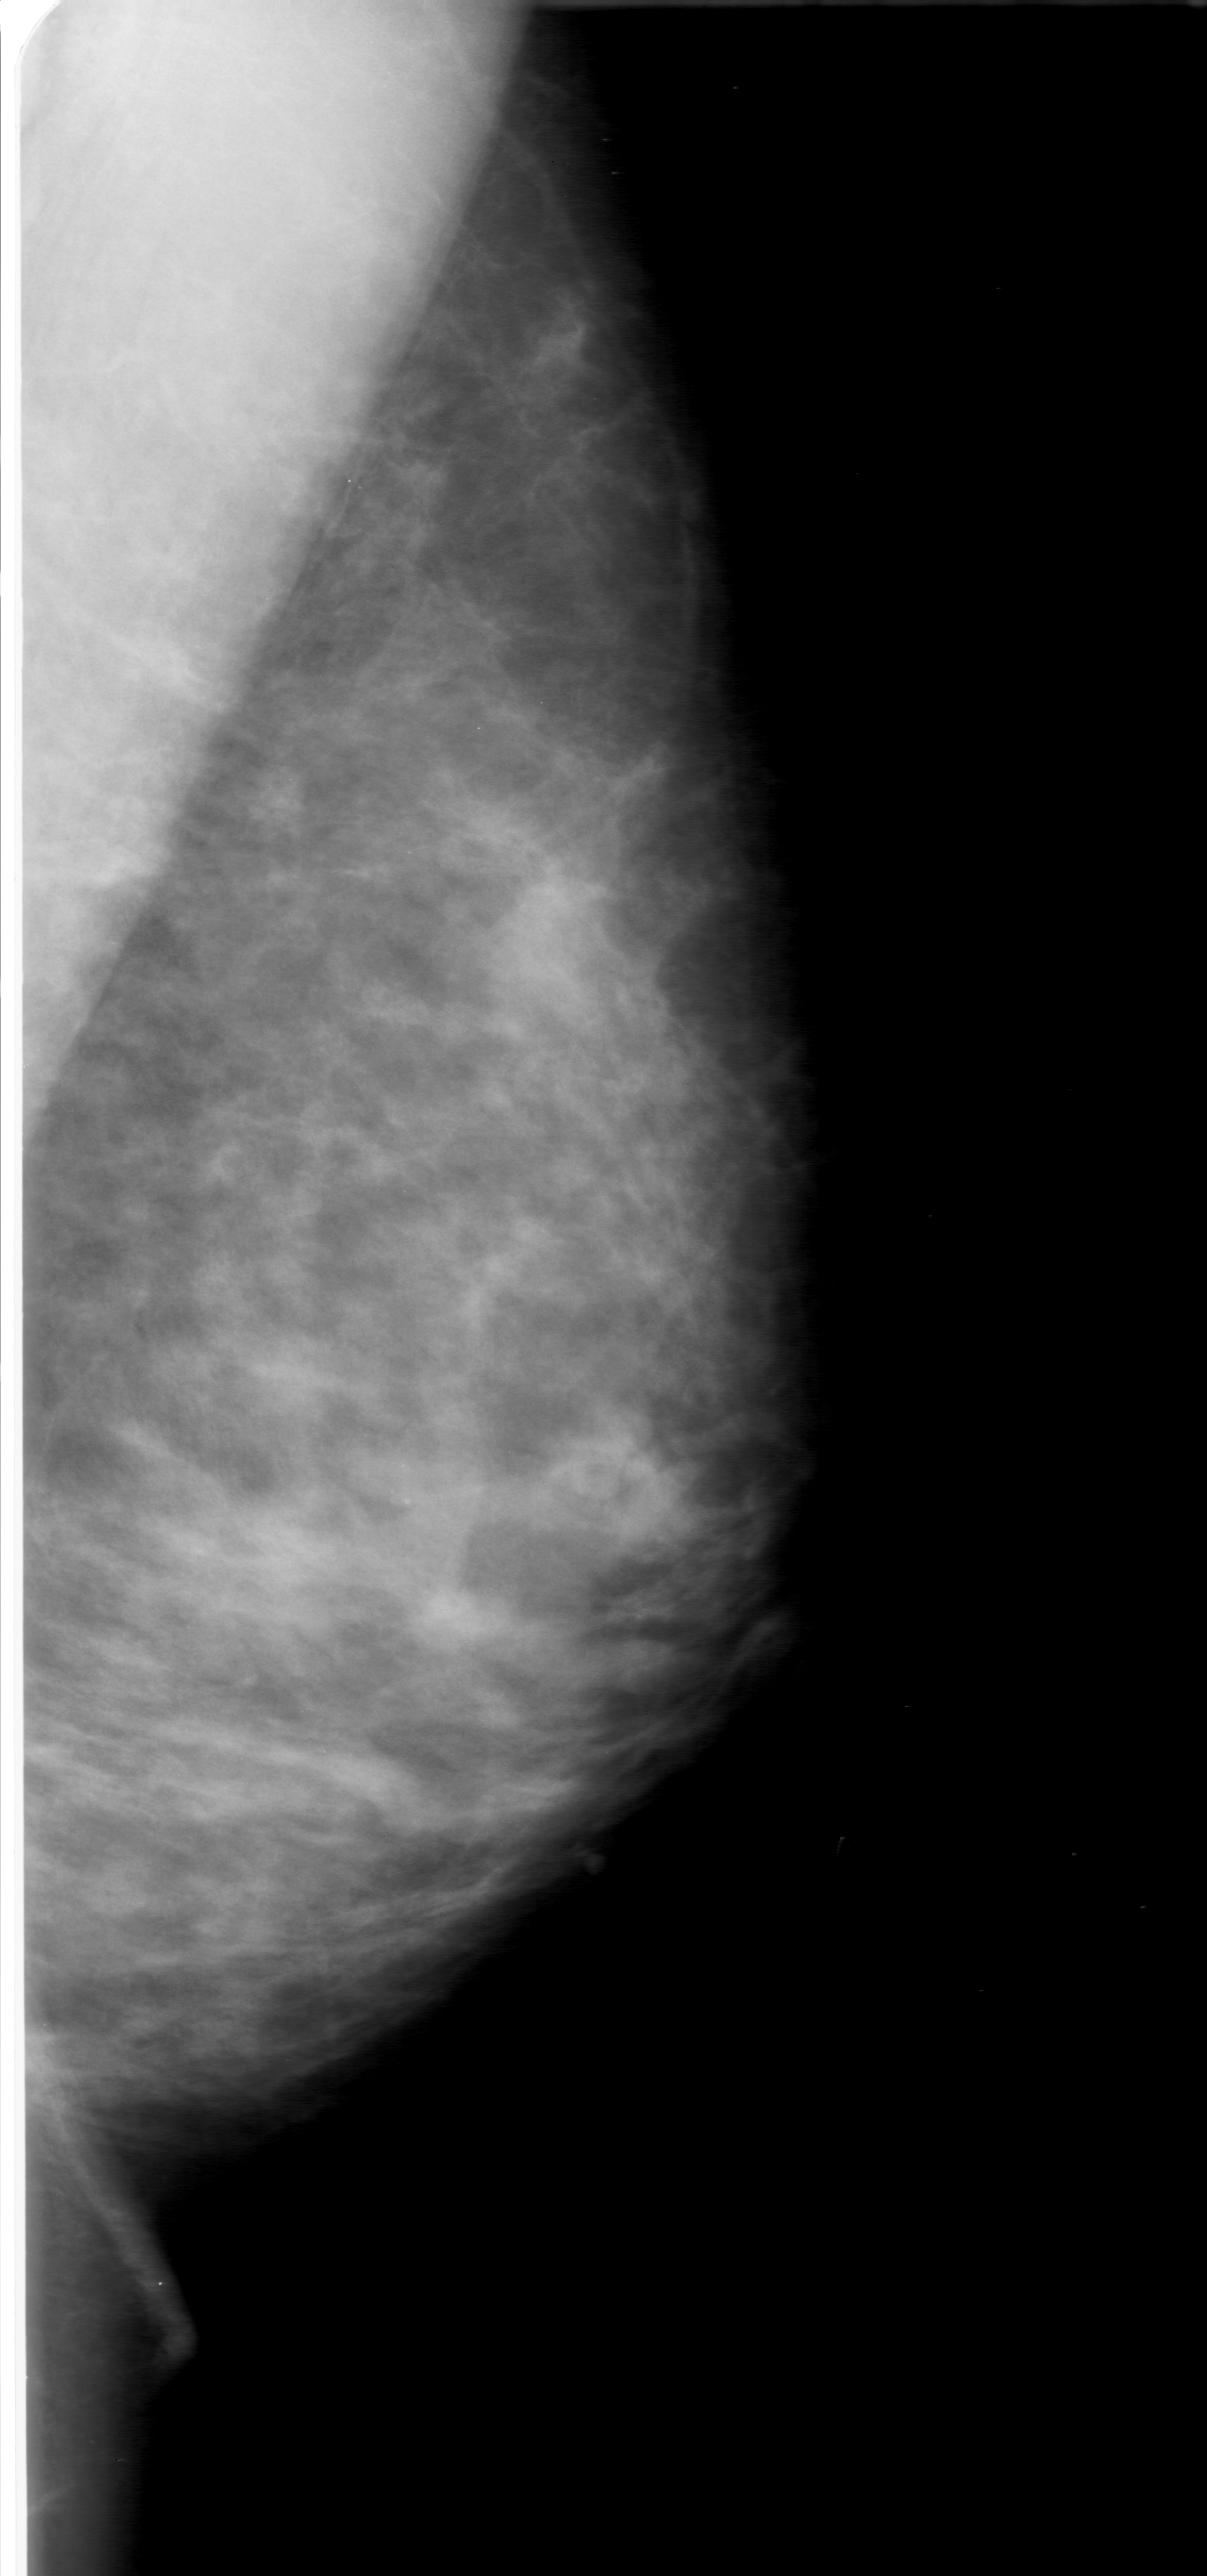
Scanned film-screen mammogram, left breast, mediolateral oblique (MLO) view, breast composition: heterogeneously dense (BI-RADS density category 3 of 4).
Mass, shape lobulated, margins microlobulated; BI-RADS assessment category 0 (incomplete: needs additional imaging); subtlety rating 3 on a 1 (subtle) to 5 (obvious) scale; pathology (as recorded): benign.